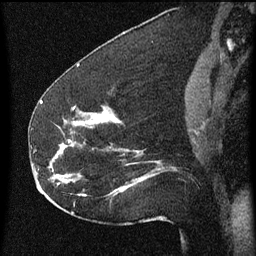
Breast MRI (dynamic contrast-enhanced), one sagittal slice. Dynamic contrast-enhanced series, image 2 of 3 at this slice position (ordered by acquisition). 1.5 T. TE 4.2 ms, TR 8 ms. 256 × 256 image matrix, field of view 180 × 180 mm. Female patient, age 52 years.
Structures marked on this image (semi-automatically segmented with operator editing):
- analysis volume of interest (the breast-tissue region the enhancement analysis was run in; not a lesion): bounding box [x1, y1, x2, y2] px = [54, 110, 175, 207]
- tumour enhancement mask (voxels above the 70 % enhancement threshold inside the analysis volume of interest): [68, 112, 129, 195]